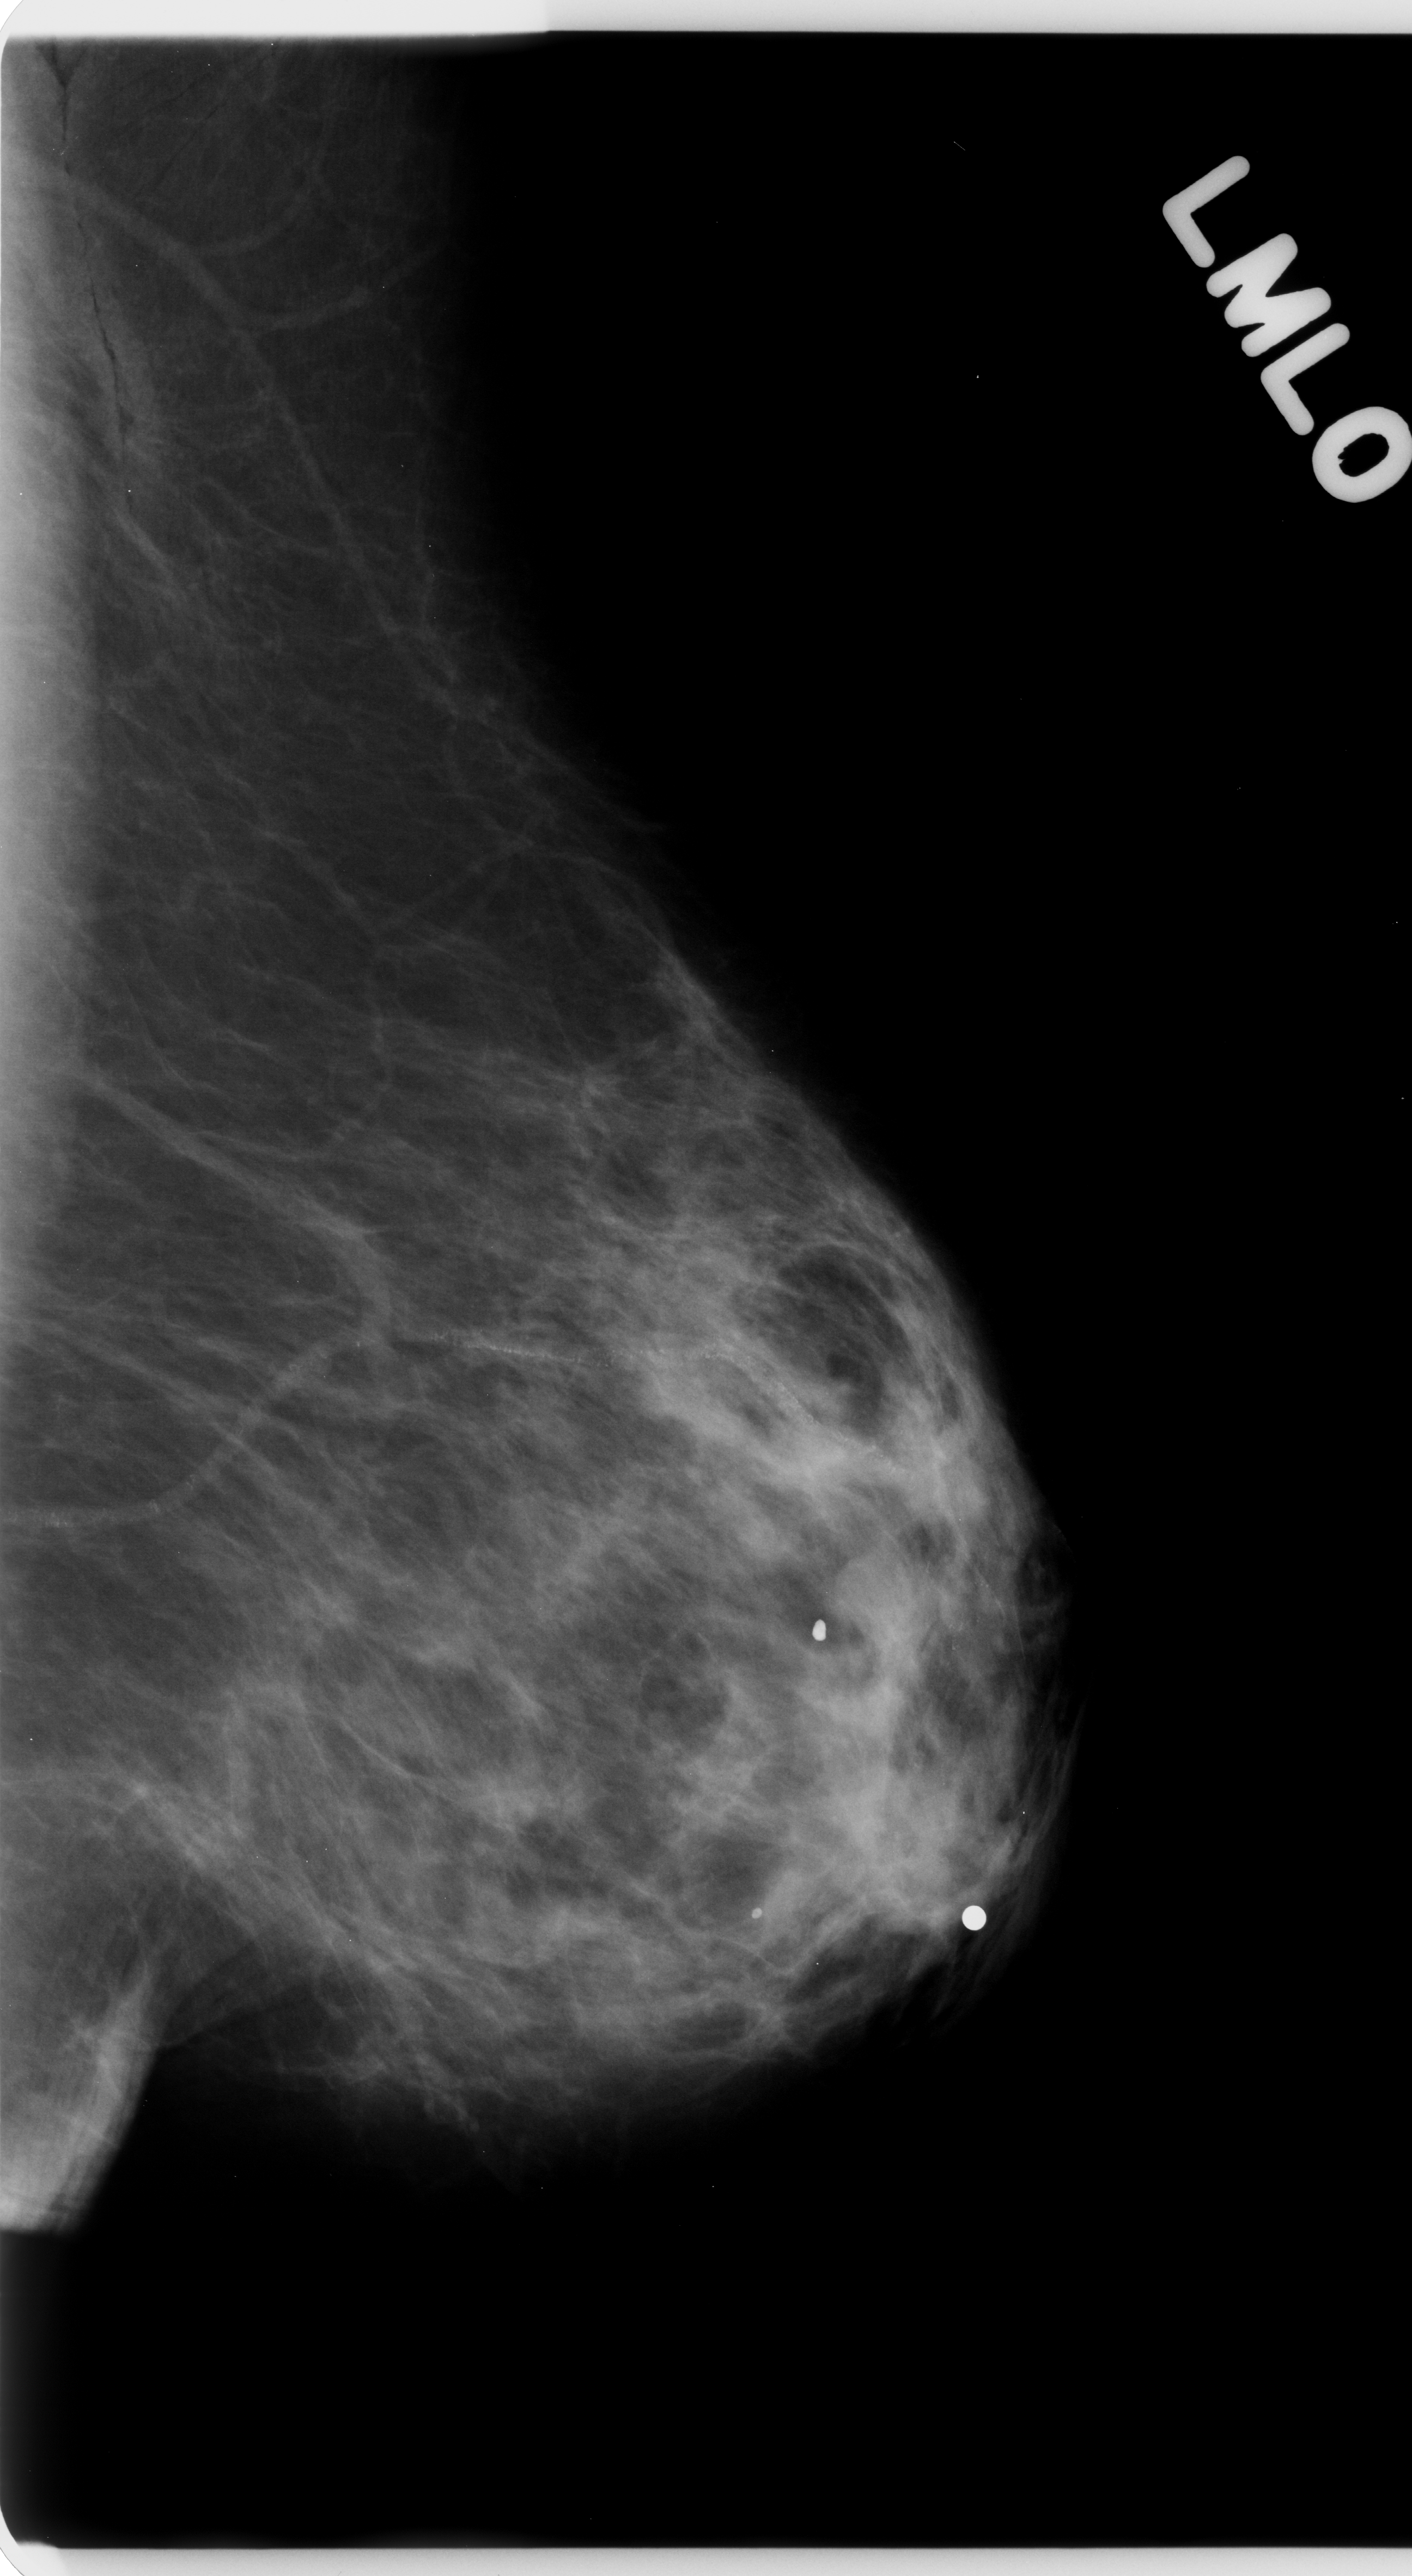
Digitized screen-film mammogram. Left breast. Mediolateral oblique (MLO) view. BI-RADS breast density category 2 (scale 1–4). 1412 × 2576 image matrix.
Marked abnormalities (boxes around the expert regions of interest):
- mass, shape lobulated, margins ill defined; BI-RADS assessment category 4; subtlety rating 3 on a 1 (subtle) to 5 (obvious) scale; pathology result (as recorded, not read from the image): malignant: box from (x=789, y=1749) to (x=976, y=1934) px